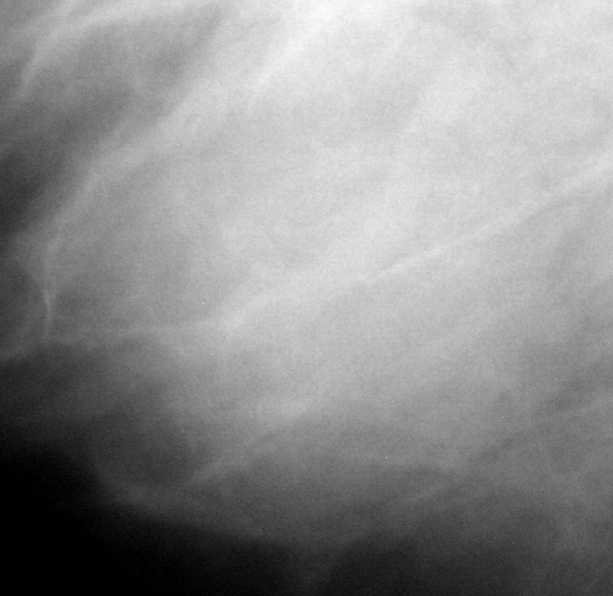
Cropped region of a digitized screen-film mammogram centred on a radiologist-marked abnormality; right breast; MLO view.
Marked abnormality: mass, shape lobulated, margins obscured; BI-RADS assessment category 3; subtlety rating 4 on a 1 (subtle) to 5 (obvious) scale; pathology result (as recorded, not read from the image): benign.